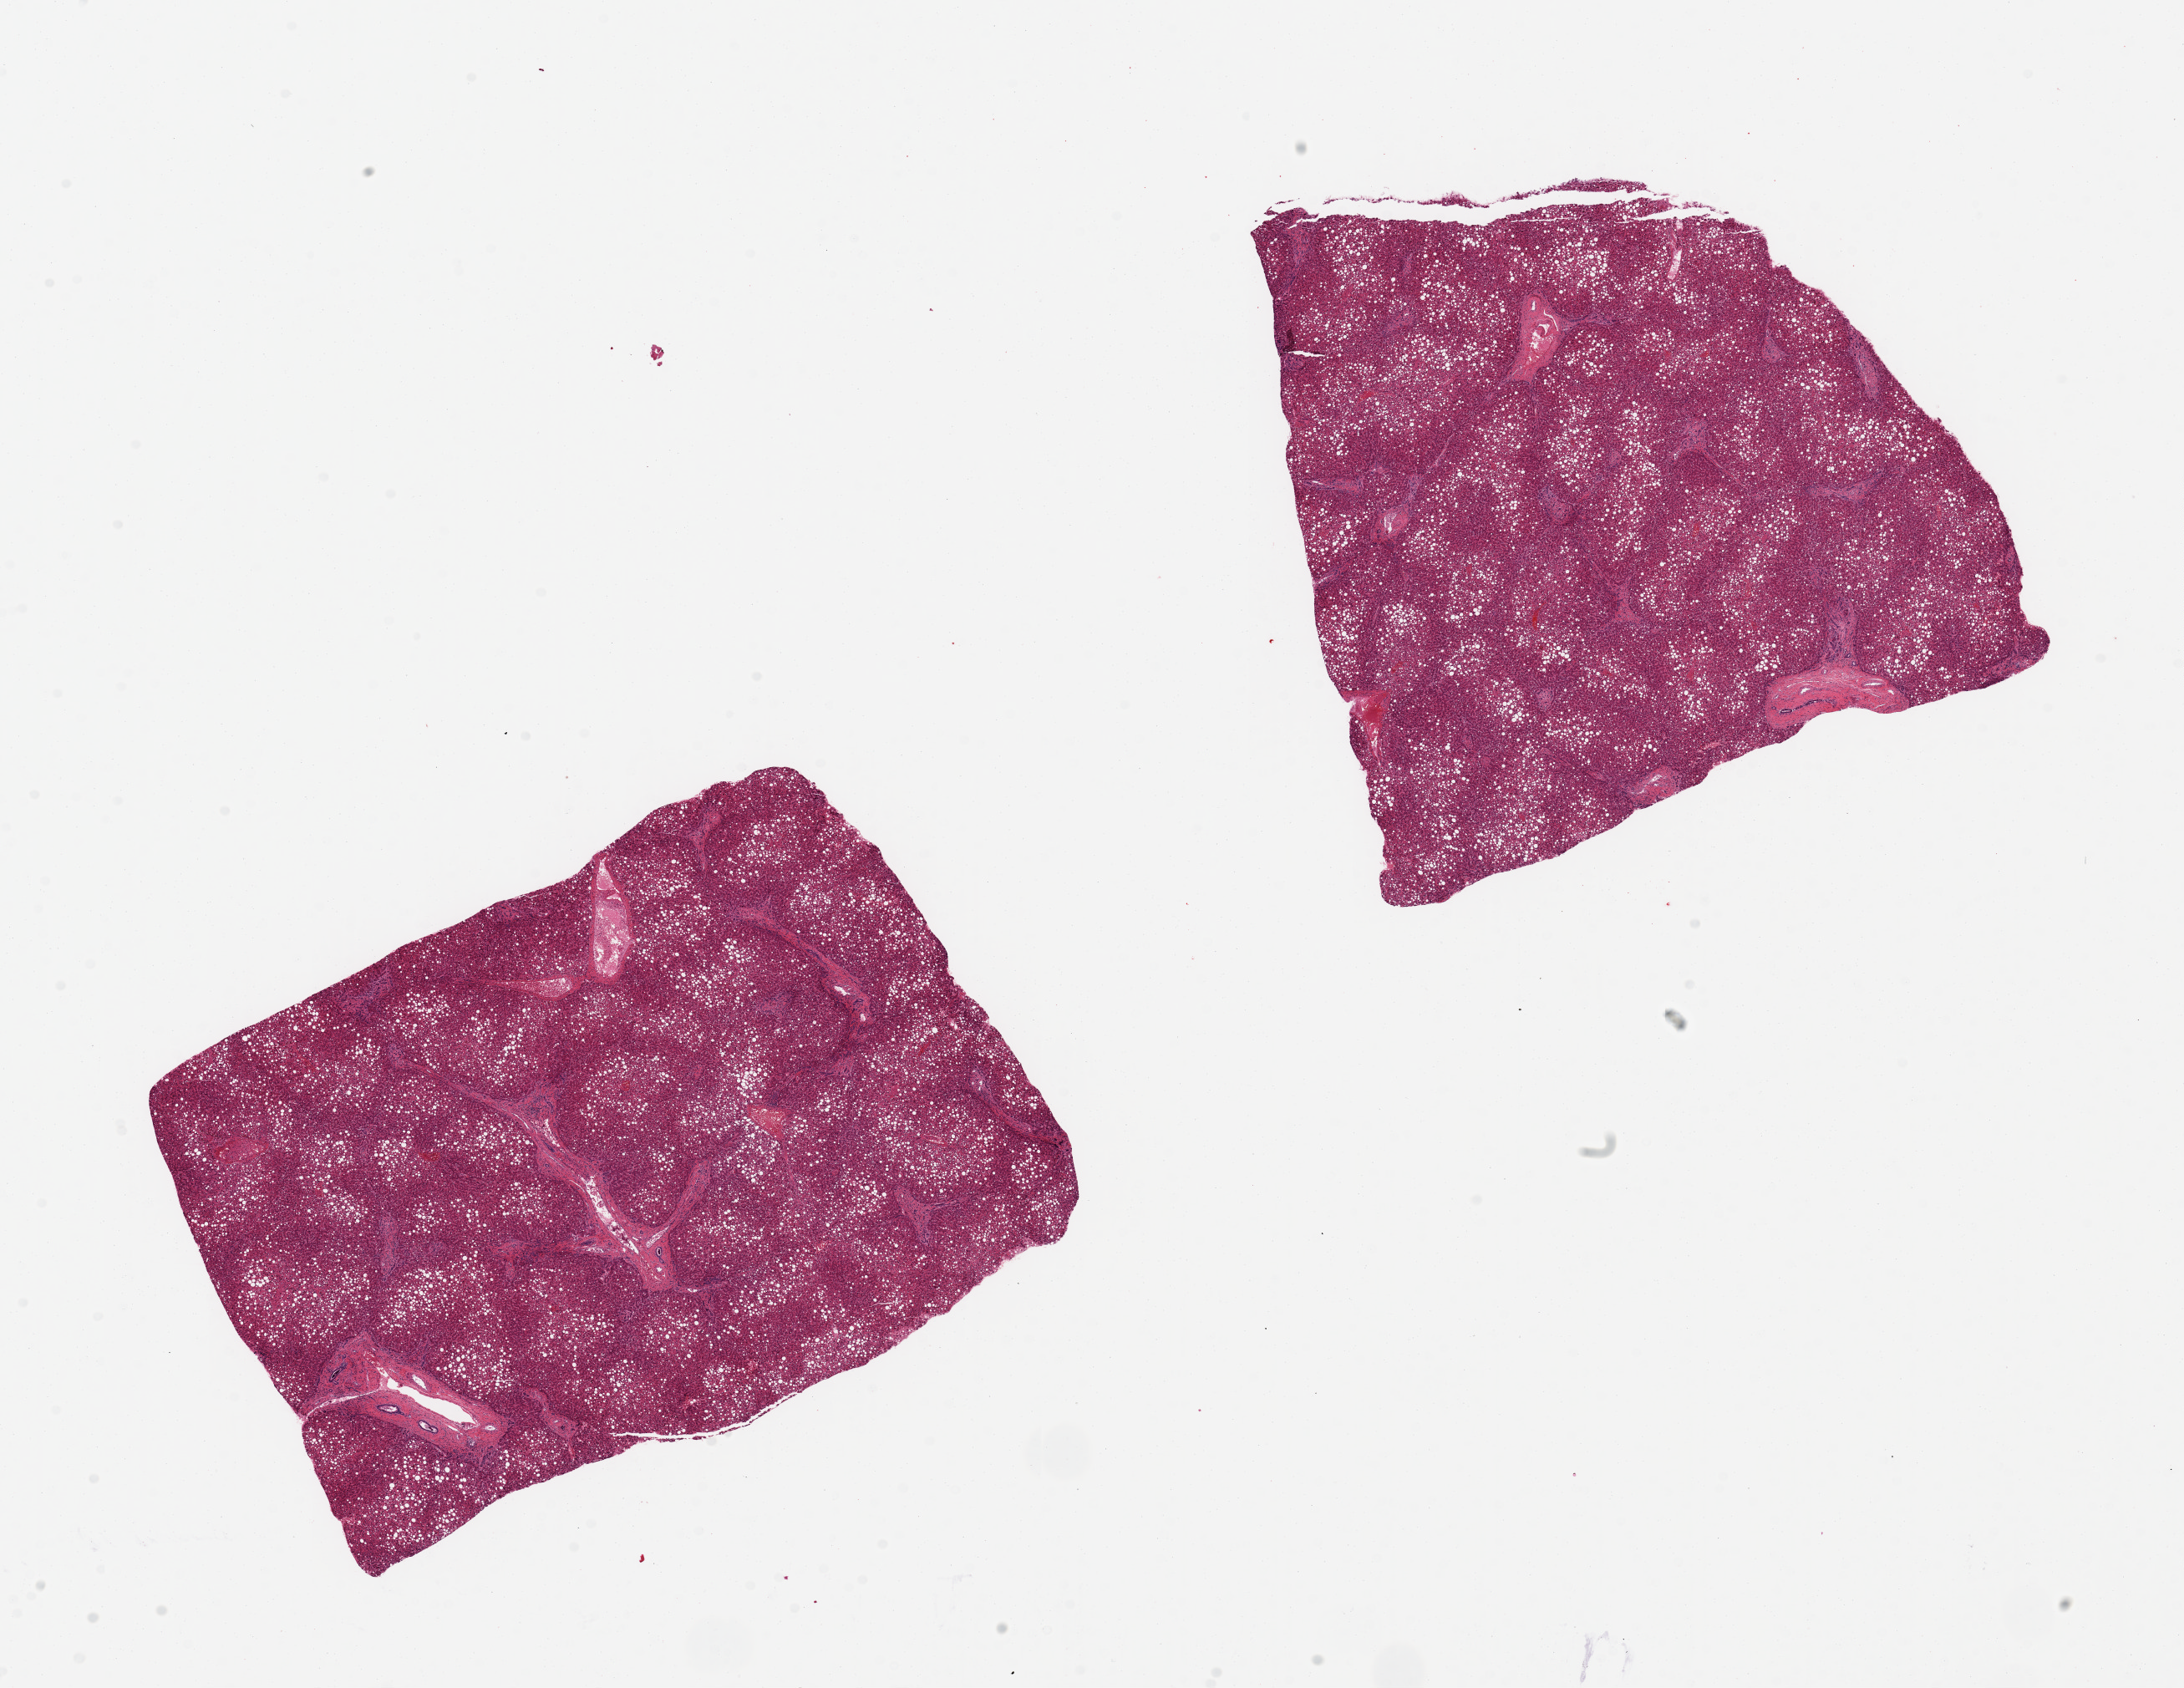
Digitized hematoxylin and eosin (H&E)-stained section, whole scanned area (about 20.7 x 16.0 mm, slide scanned at 20x) shown as a low-resolution overview; PAXgene-fixed, paraffin-embedded tissue; section of liver (target tissue); tissue donor sample. Donor sex: male.
Review note (as recorded): 2 pieces ~7x6mm. Diffuse macrovesicular steatosis involves 50-60% of parenchyma, with focal early bridging fibrosis.